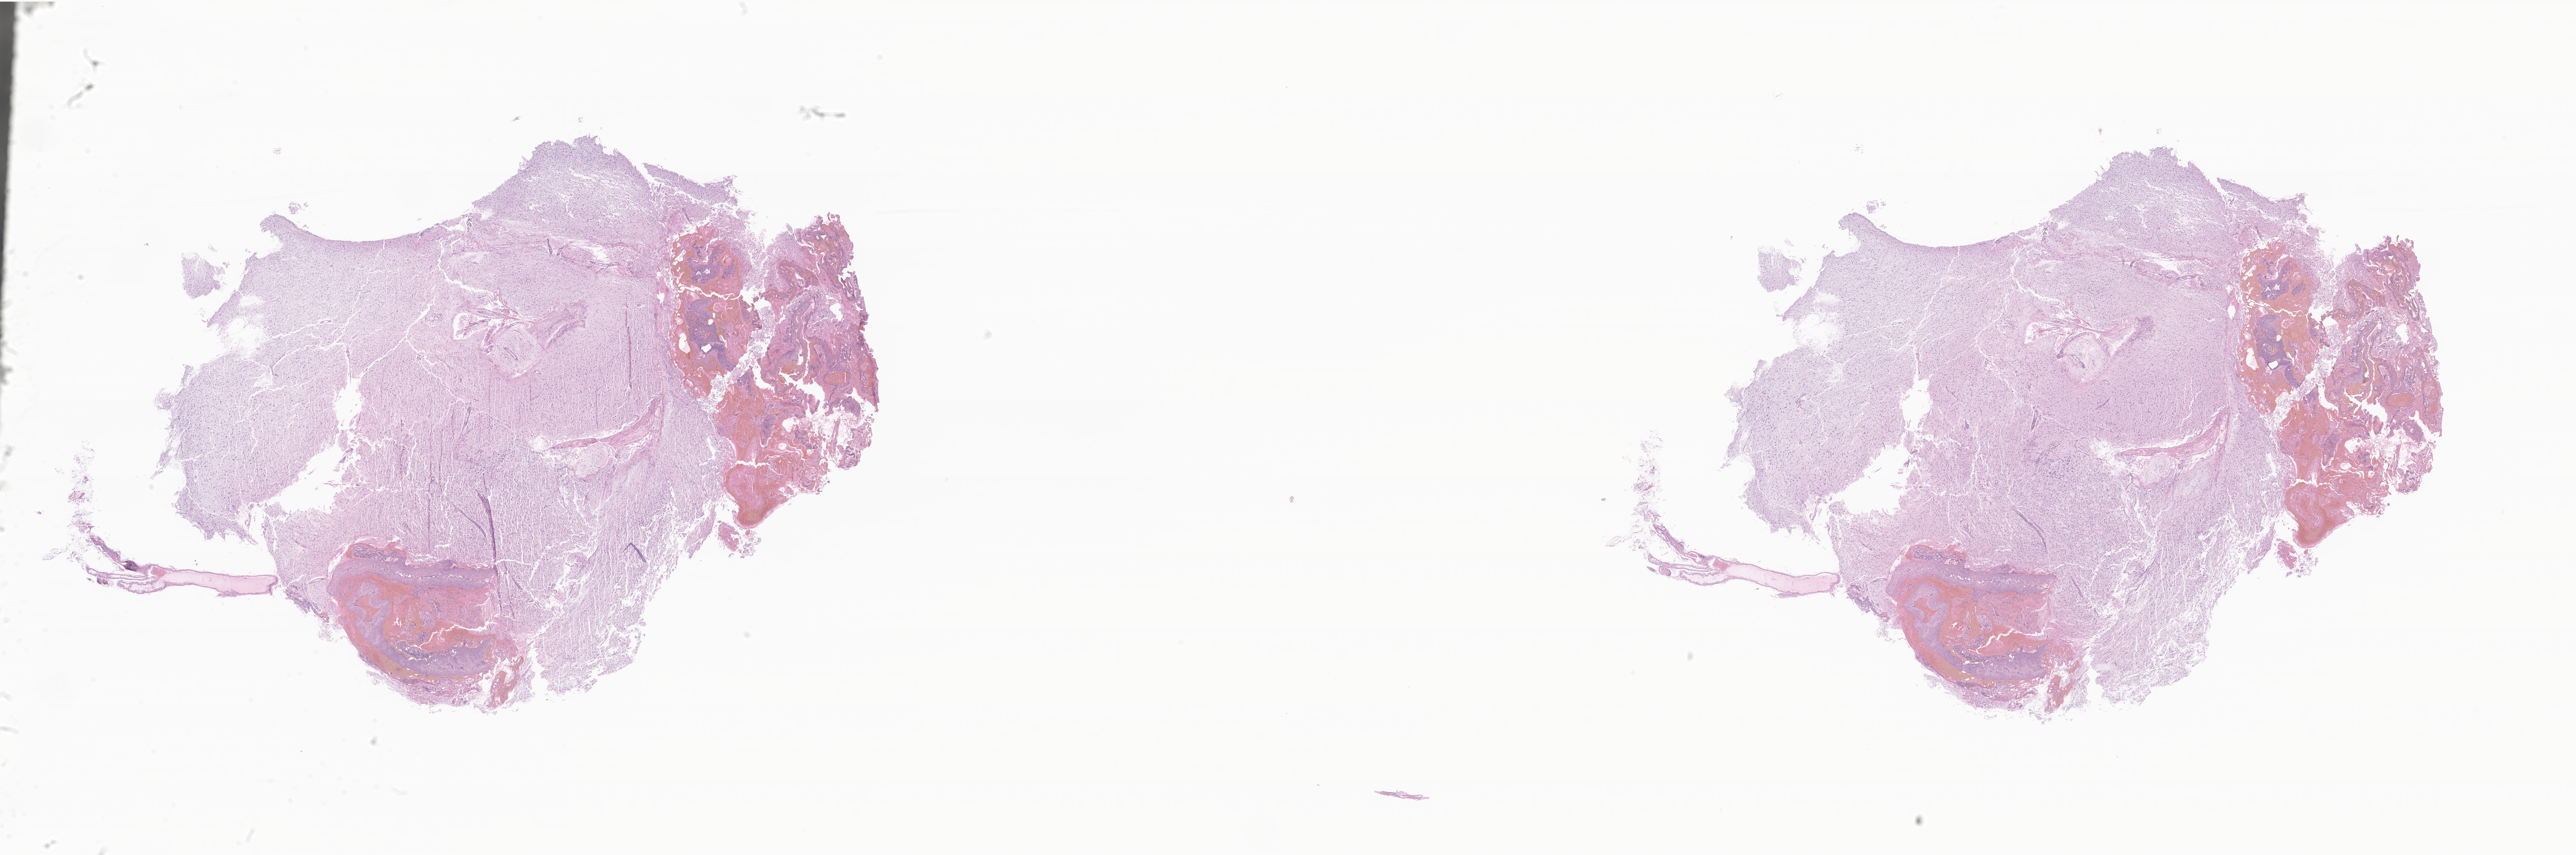
Whole-slide image, H&E stain of tumor tissue from the parietal lobe — whole scanned area (about 36.1 x 12.0 mm) shown as a low-resolution overview; FFPE section. Male patient, age 125 months (10 years 5 months).
Recorded diagnosis: Dysembryoplastic neuroepithelial tumor.